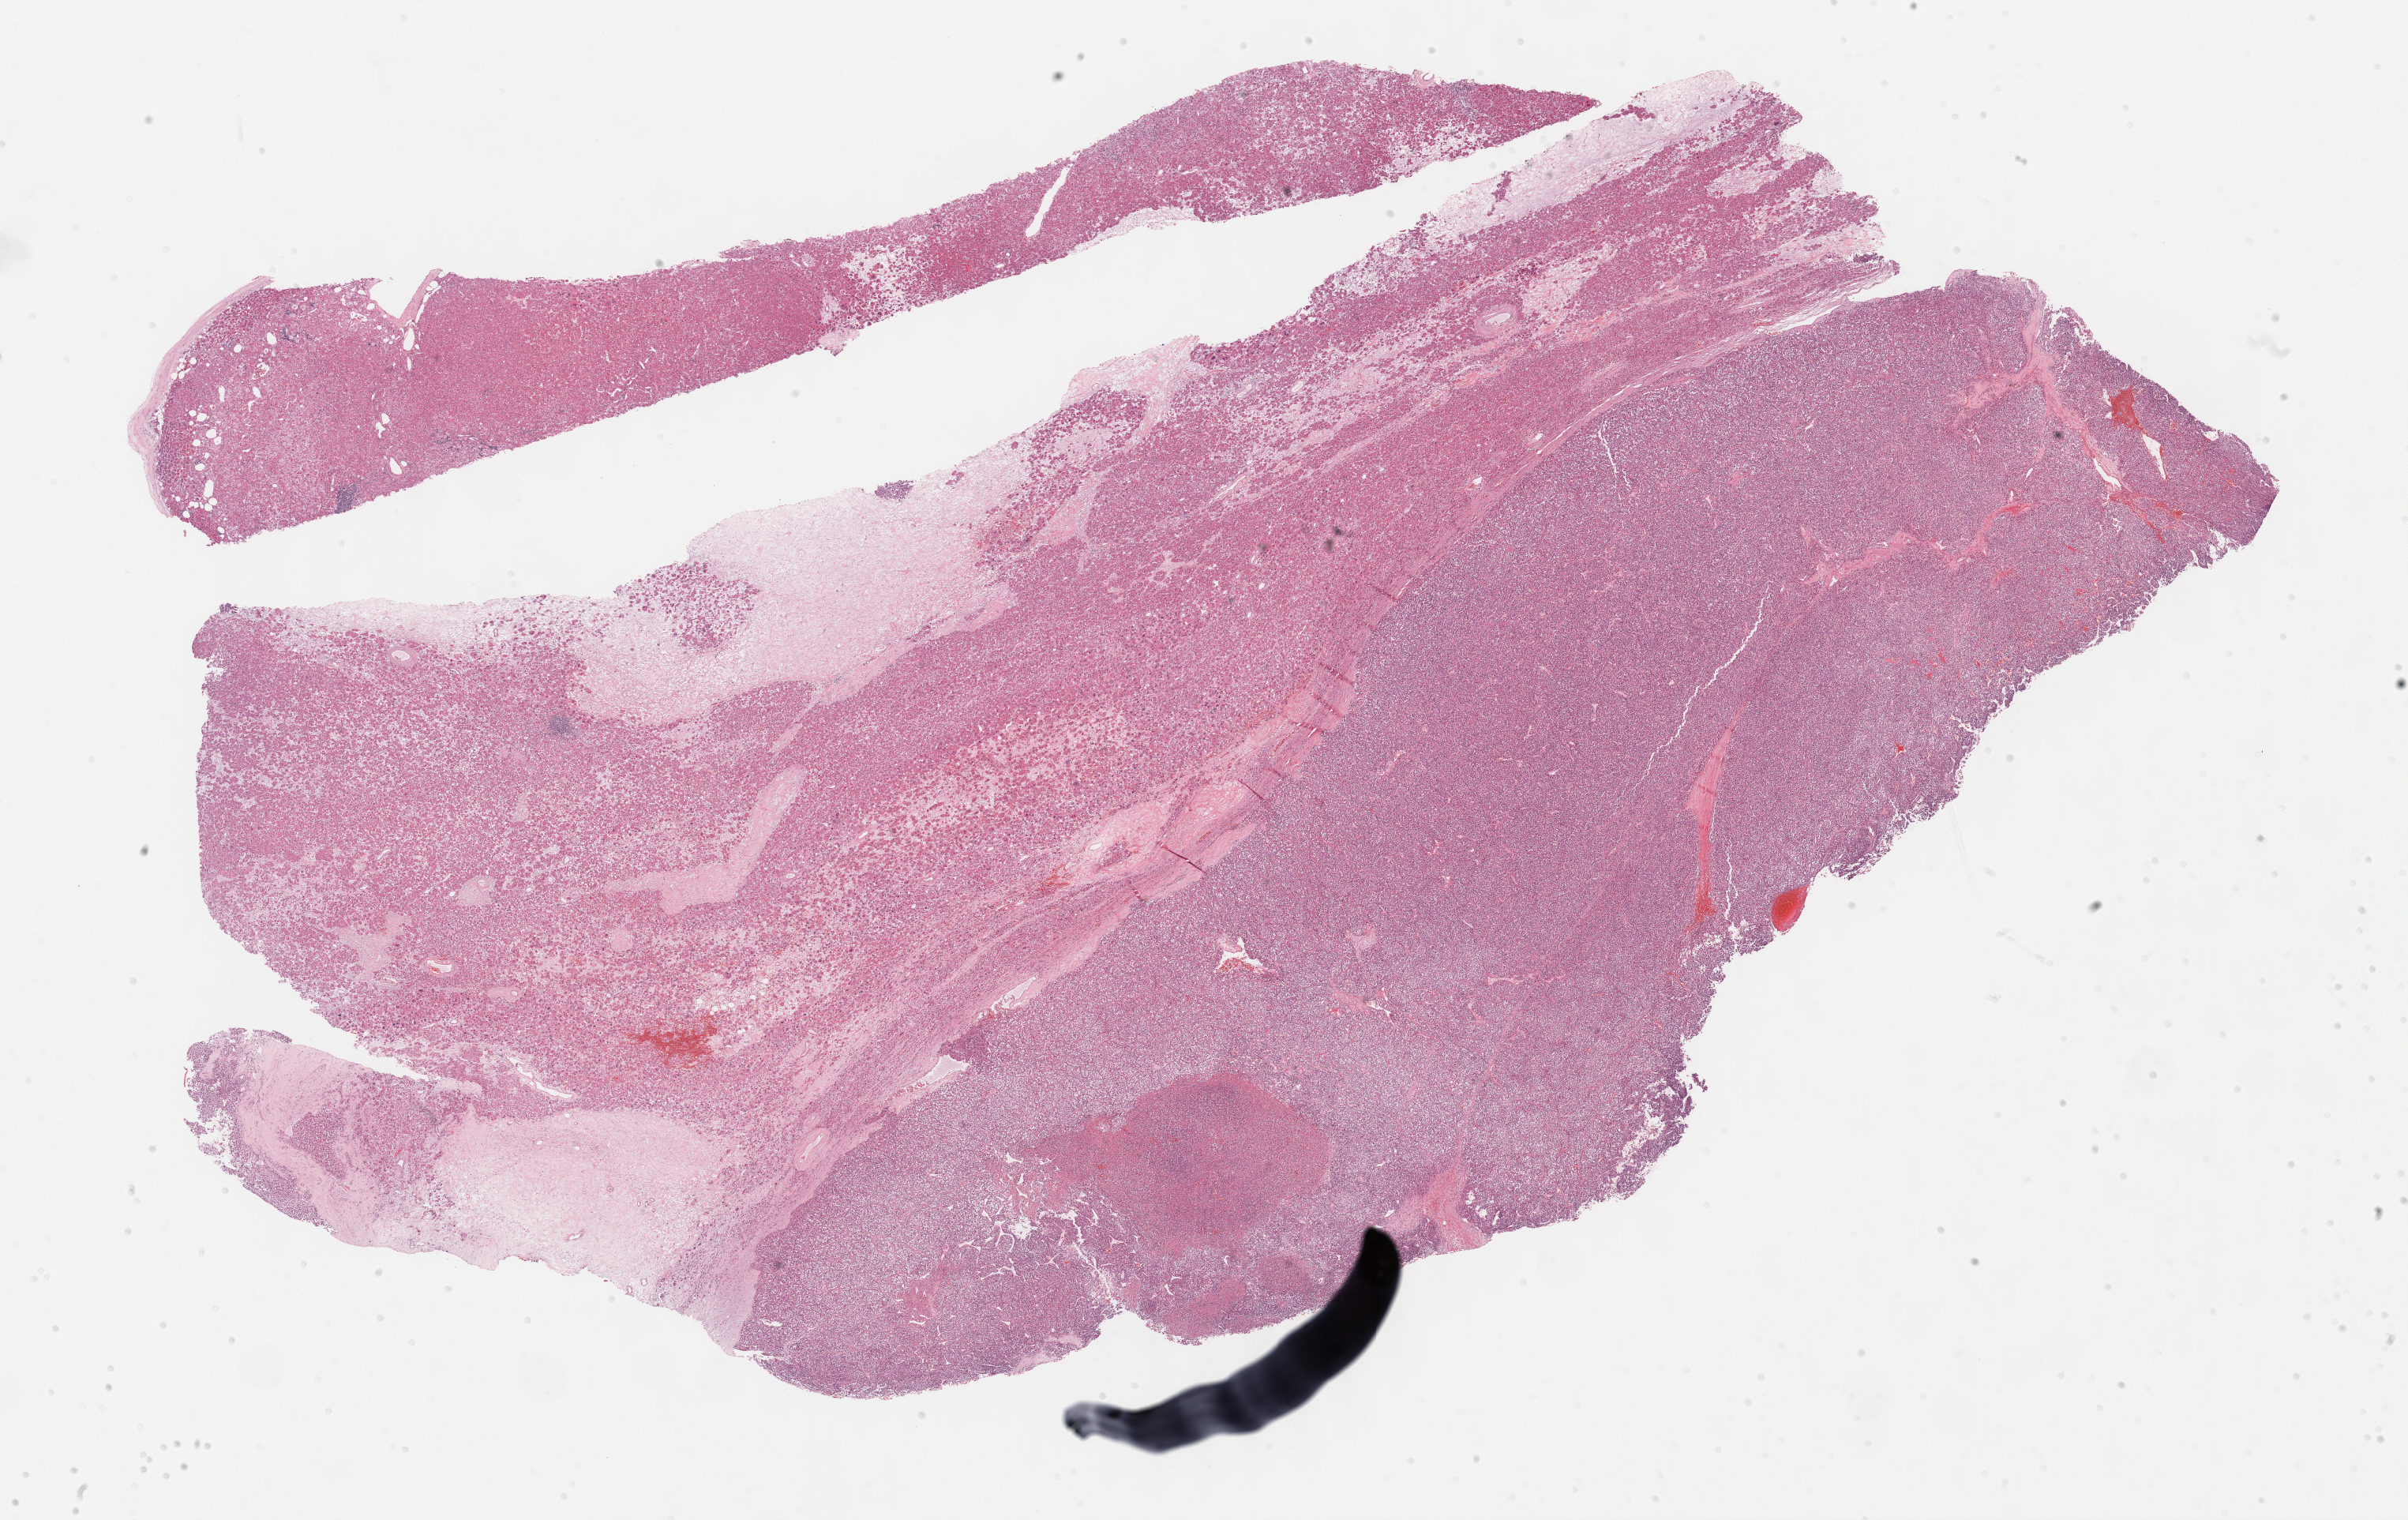
Whole-slide histology image, H&E-stained, shown as a low-resolution overview of the whole scanned area (about 24.7 x 15.6 mm); formalin-fixed paraffin-embedded (FFPE) diagnostic section; sample: primary tumour, adrenal cortex. Male, age 60 years at initial diagnosis.
• pathologic diagnosis: Adrenal cortical carcinoma (cortex of adrenal gland)